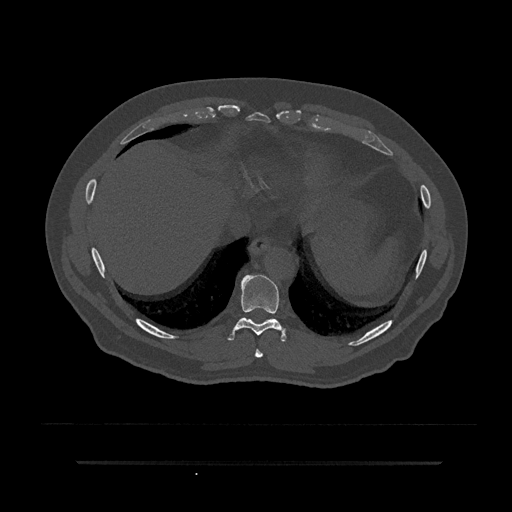
CT including the spine, one axial slice; slice 374 of 797 in the series (ordered by position); reconstruction kernel Br40s/3; 120 kVp; bone window (W 1800 / L 400 HU); 0.5 mm slice thickness; 512 × 512 image matrix, field of view 464 × 464 mm. Male patient, age 59 years. Case-level facts recorded for this patient, not image findings: primary cancer: bile ducts.
Annotated regions visible in this slice (semi-automatically segmented with operator editing):
- T8 vertebra: bounding box [x1, y1, x2, y2] px = [255, 349, 263, 358]
- T9 vertebra: [227, 275, 286, 342]